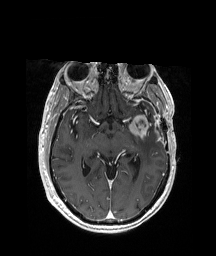
Brain MRI from a brain-tumour surgery series, one axial slice; slice 117 of 208 in the series (ordered by position); T1-weighted post-contrast; 216 × 256 image matrix, field of view 228 × 270 mm. Case-level facts recorded for this patient, not image findings: histopathology: Glioblastoma; WHO grade: 4; IDH mutation: no.
Structures marked on this image (outlined manually by an expert reader):
- previous resection cavity: bounding box <136,125,138,127> (left, top, right, bottom; pixels)
- tumour: <123,113,158,139>